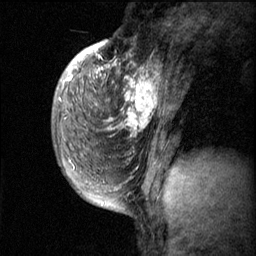
Breast MRI (dynamic contrast-enhanced), one sagittal slice. Position 17 of 60 along the scan axis. Dynamic contrast-enhanced series, image 2 of 3 at this slice position (ordered by acquisition). 1.5 T. TE 4.2 ms, TR 11.1 ms. 256 × 256 image matrix, field of view 180 × 180 mm. Patient: female, 50 years.
Outlined on this slice (semi-automatically segmented with operator editing):
- analysis volume of interest (the breast-tissue region the enhancement analysis was run in; not a lesion): bounding box (x1, y1, x2, y2) in pixels: (82, 56, 168, 143)
- tumour enhancement mask (voxels above the 70 % enhancement threshold inside the analysis volume of interest): (82, 56, 160, 133)